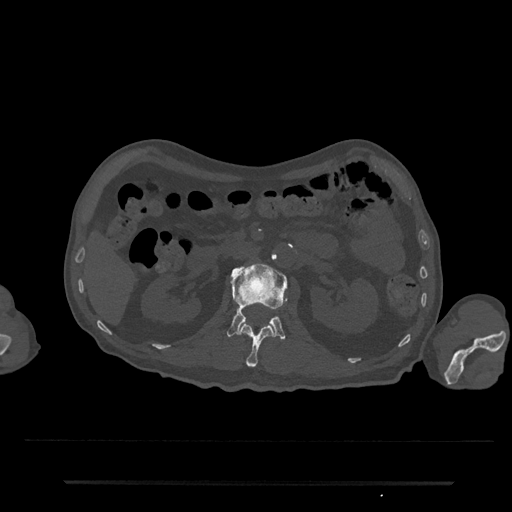
CT including the spine, one axial slice; position 94 of 797 along the scan axis; reconstruction kernel Br40s/3; 120 kVp; bone window (W 1800 / L 400 HU); 0.5 mm slice thickness; 512 × 512 image matrix, field of view 427 × 427 mm. Male patient, age 74 years. From the clinical record (not read from this slice): primary cancer: prostate.
Structures marked on this image (semi-automatically segmented with operator editing):
- L1 vertebra: bounding box [x1, y1, x2, y2] px = [238, 323, 274, 367]
- L2 vertebra: [227, 263, 287, 339]